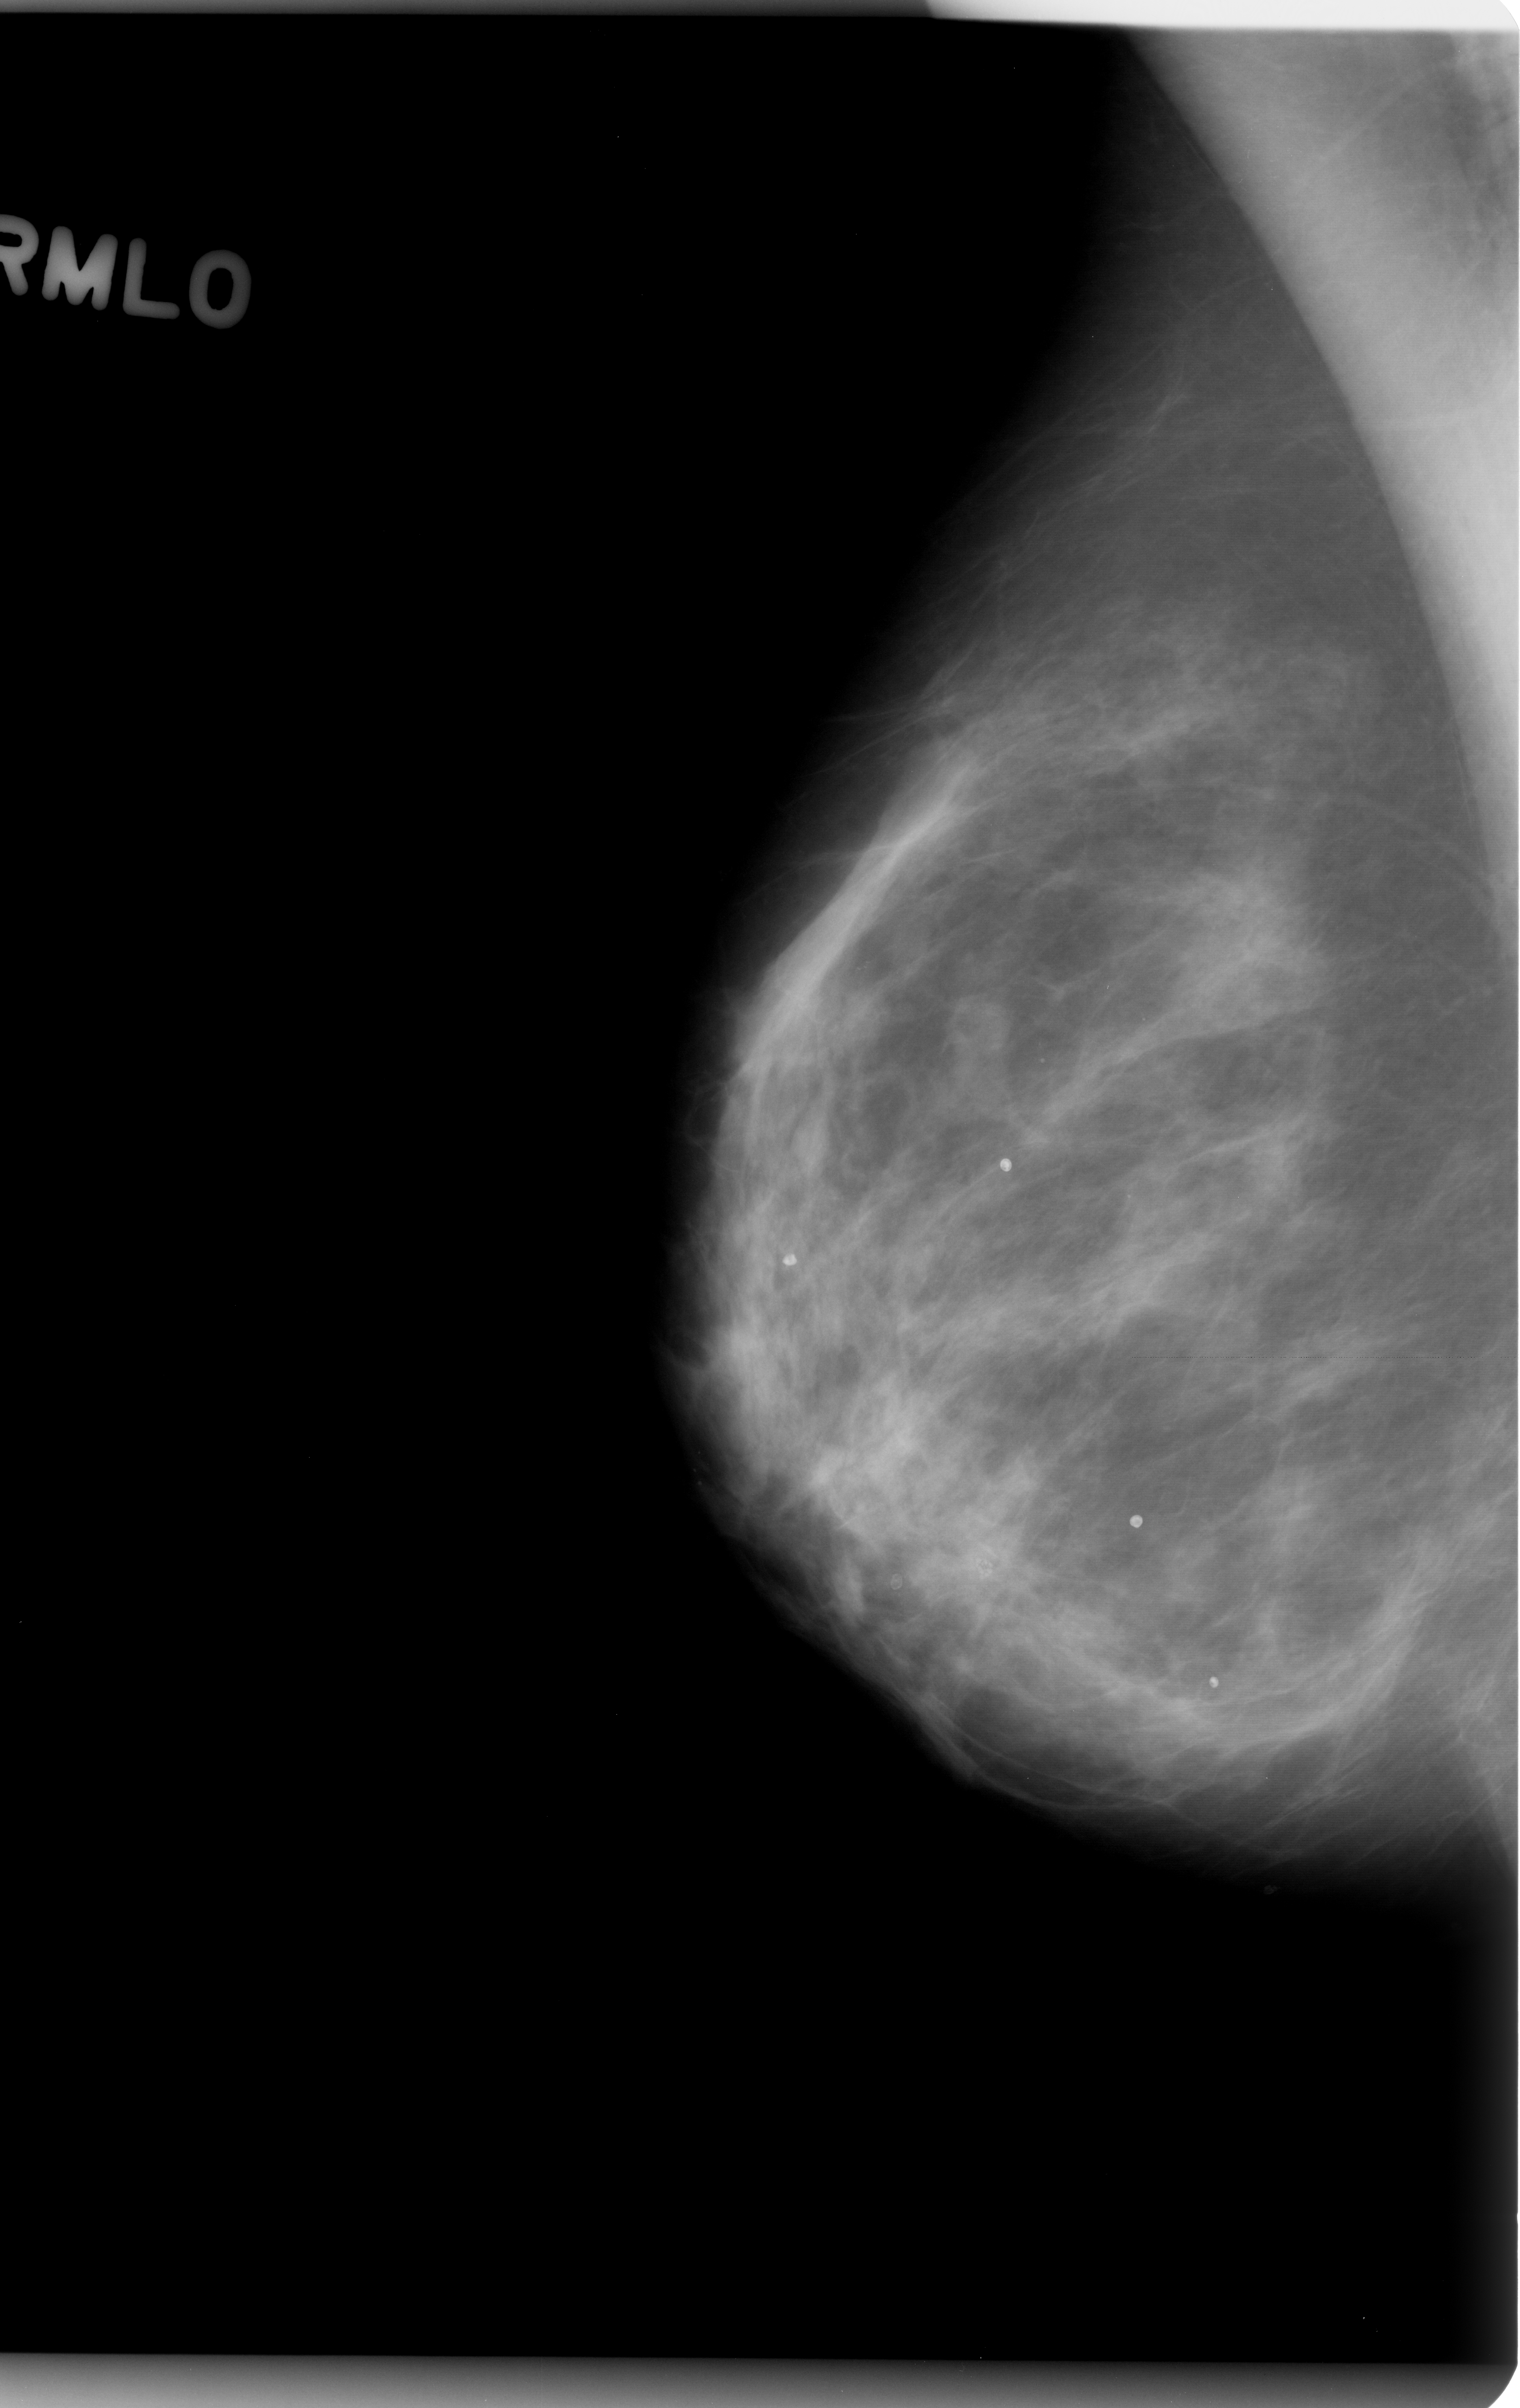
Digitized screen-film mammogram. Right breast. Mediolateral oblique (MLO) view. Breast composition: scattered fibroglandular densities (BI-RADS density category 2 of 4). 1520 × 2408 image matrix.
Marked abnormalities (boxes around the expert regions of interest):
- mass, shape round, margins obscured; BI-RADS assessment category 3; subtlety rating 3 on a 1 (subtle) to 5 (obvious) scale; pathology (as recorded): benign: bounding box [x1, y1, x2, y2] px = [913, 991, 1034, 1123]